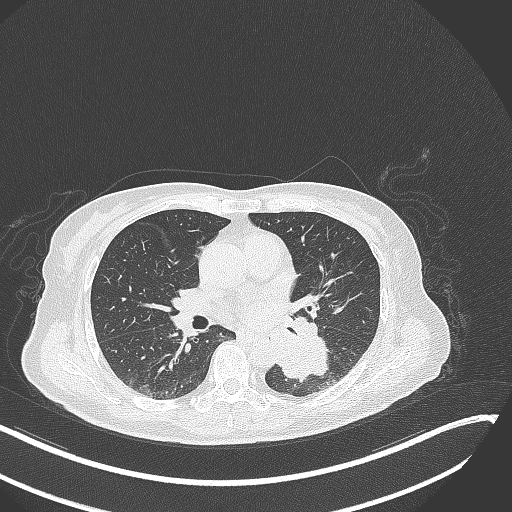
Chest CT, one axial slice. Reconstruction kernel B70f. 120 kVp. Lung window (W 1500 / L -600 HU). 1 mm slice thickness. 512 × 512 image matrix, field of view 400 × 400 mm. Patient: female, 64 years. From the clinical record (not read from this slice): clinical TNM (as recorded): T3 N1 M1.
Annotated regions visible in this slice (rectangle marked by the reading radiologist):
- lung tumour (recorded histology: small cell carcinoma): box from (x=265, y=326) to (x=329, y=382) px